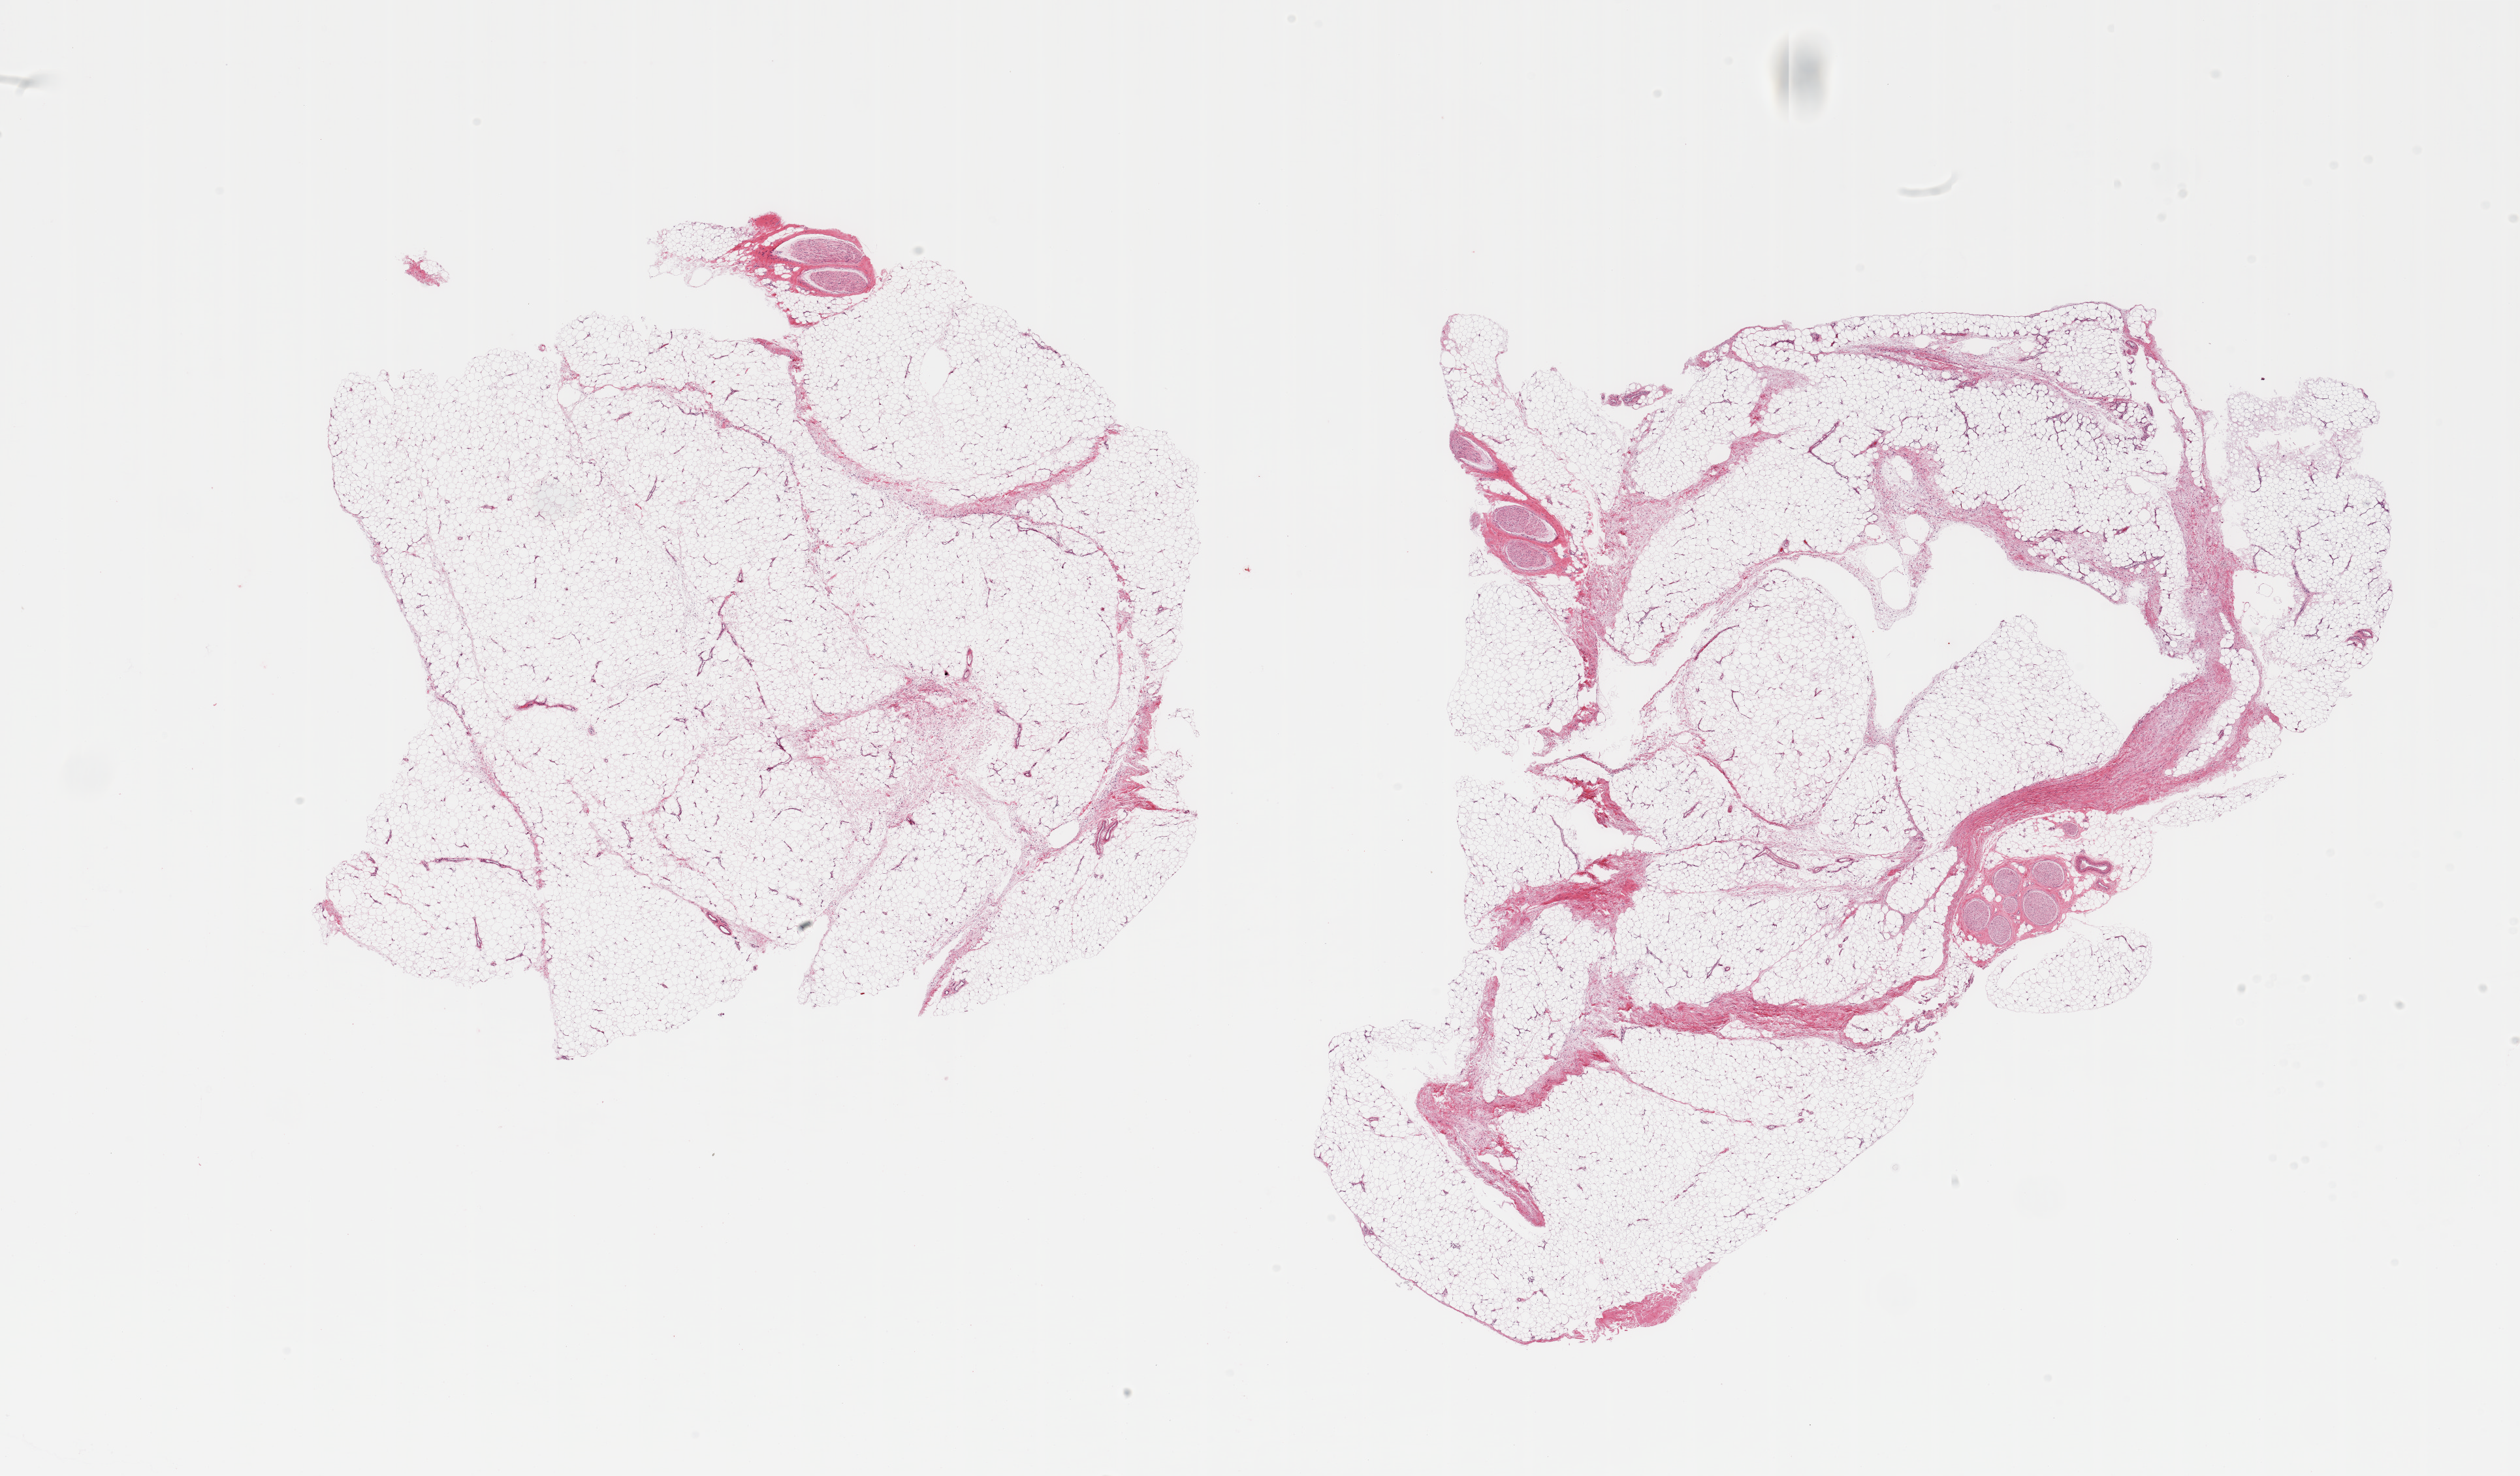
Whole-slide image, hematoxylin and eosin (H&E) stain — whole scanned area (about 30.5 x 17.9 mm) shown as a low-resolution overview. PAXgene-fixed paraffin-embedded (PFPE) section. Section of adipose tissue (target tissue). Donor tissue sample.
Pathologist's review note for this sample: 2 pieces; 5% and 10% fibrovascular component and nerves.